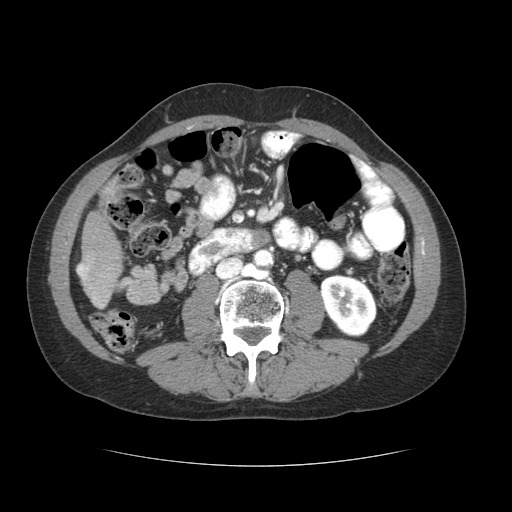
Contrast-enhanced abdominal CT (liver protocol), one axial slice; position 9 of 69 along the scan axis; reconstruction kernel STANDARD; 120 kVp; soft-tissue window (W 400 / L 40 HU); 2.5 mm slice thickness; 512 × 512 image matrix, field of view 360 × 360 mm. From the clinical record (not read from this slice): diagnosis: hepatocellular carcinoma (patient treated with transarterial chemoembolisation; whether this scan precedes or follows treatment is not stated here); TNM stage (as recorded): Stage-II.
Annotated regions visible in this slice (semi-automatic segmentation, software-assisted and operator-edited):
- liver parenchyma outside the tumour (the mass and vessels are separate outlines, so this box may not span the whole liver): box from (x=76, y=179) to (x=122, y=308) px
- liver vessels: (x=77, y=264)–(x=103, y=307)